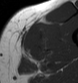
MRI of an extremity soft-tissue mass, one axial slice. Position 28 of 43 along the scan axis. MR volume resampled by the dataset authors to the PET/CT grid (not the native acquisition matrix). 78 × 83 image matrix. Male patient. Case-level facts recorded for this patient, not image findings: histological type: pleiomorphic leiomyosarcoma; grade: high; site of the primary tumour: left thigh.
Structures marked on this image (expert contour drawn on MRI and transferred to this co-registered scan by the dataset authors):
- gross tumour volume including surrounding oedema: bounding box (x1, y1, x2, y2) in pixels: (20, 24, 51, 61)
- gross tumour volume (mass): (24, 30, 44, 59)